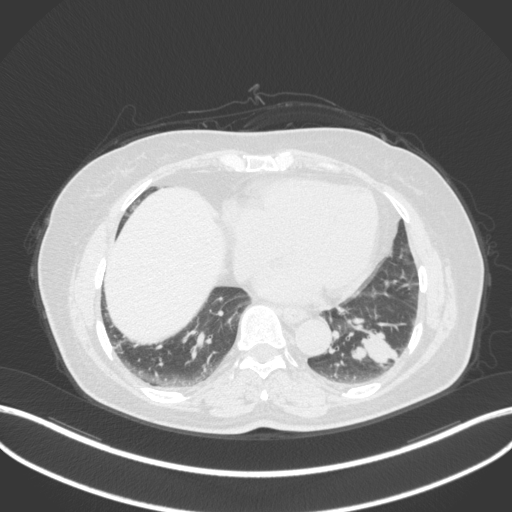
Chest CT, one axial slice. Position 128 of 307 along the scan axis. Reconstruction kernel B31f. 120 kVp. Lung window (W 1500 / L -600 HU). 1 mm slice thickness. 512 × 512 image matrix. Female patient, age 59 years. Case-level facts recorded for this patient, not image findings: clinical TNM (as recorded): T2a N0 M0; histopathological grade: G2-3.
Structures marked on this image (rectangle marked by the reading radiologist):
- lung tumour (recorded histology: adenocarcinoma): bounding box [x1, y1, x2, y2] px = [345, 328, 401, 368]